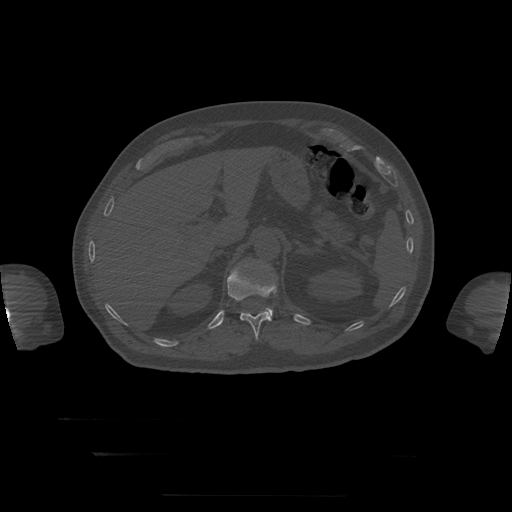
CT including the spine, one axial slice; position 68 of 397 along the scan axis; 120 kVp; bone window (W 1800 / L 400 HU); 1.25 mm slice thickness; 512 × 512 image matrix. Patient age 73 years. Case-level facts recorded for this patient, not image findings: primary cancer: prostate.
Outlined on this slice (semi-automatically segmented with operator editing):
- L1 vertebra: box from (x=266, y=308) to (x=273, y=319) px
- T12 vertebra: (x=228, y=268)–(x=277, y=339)